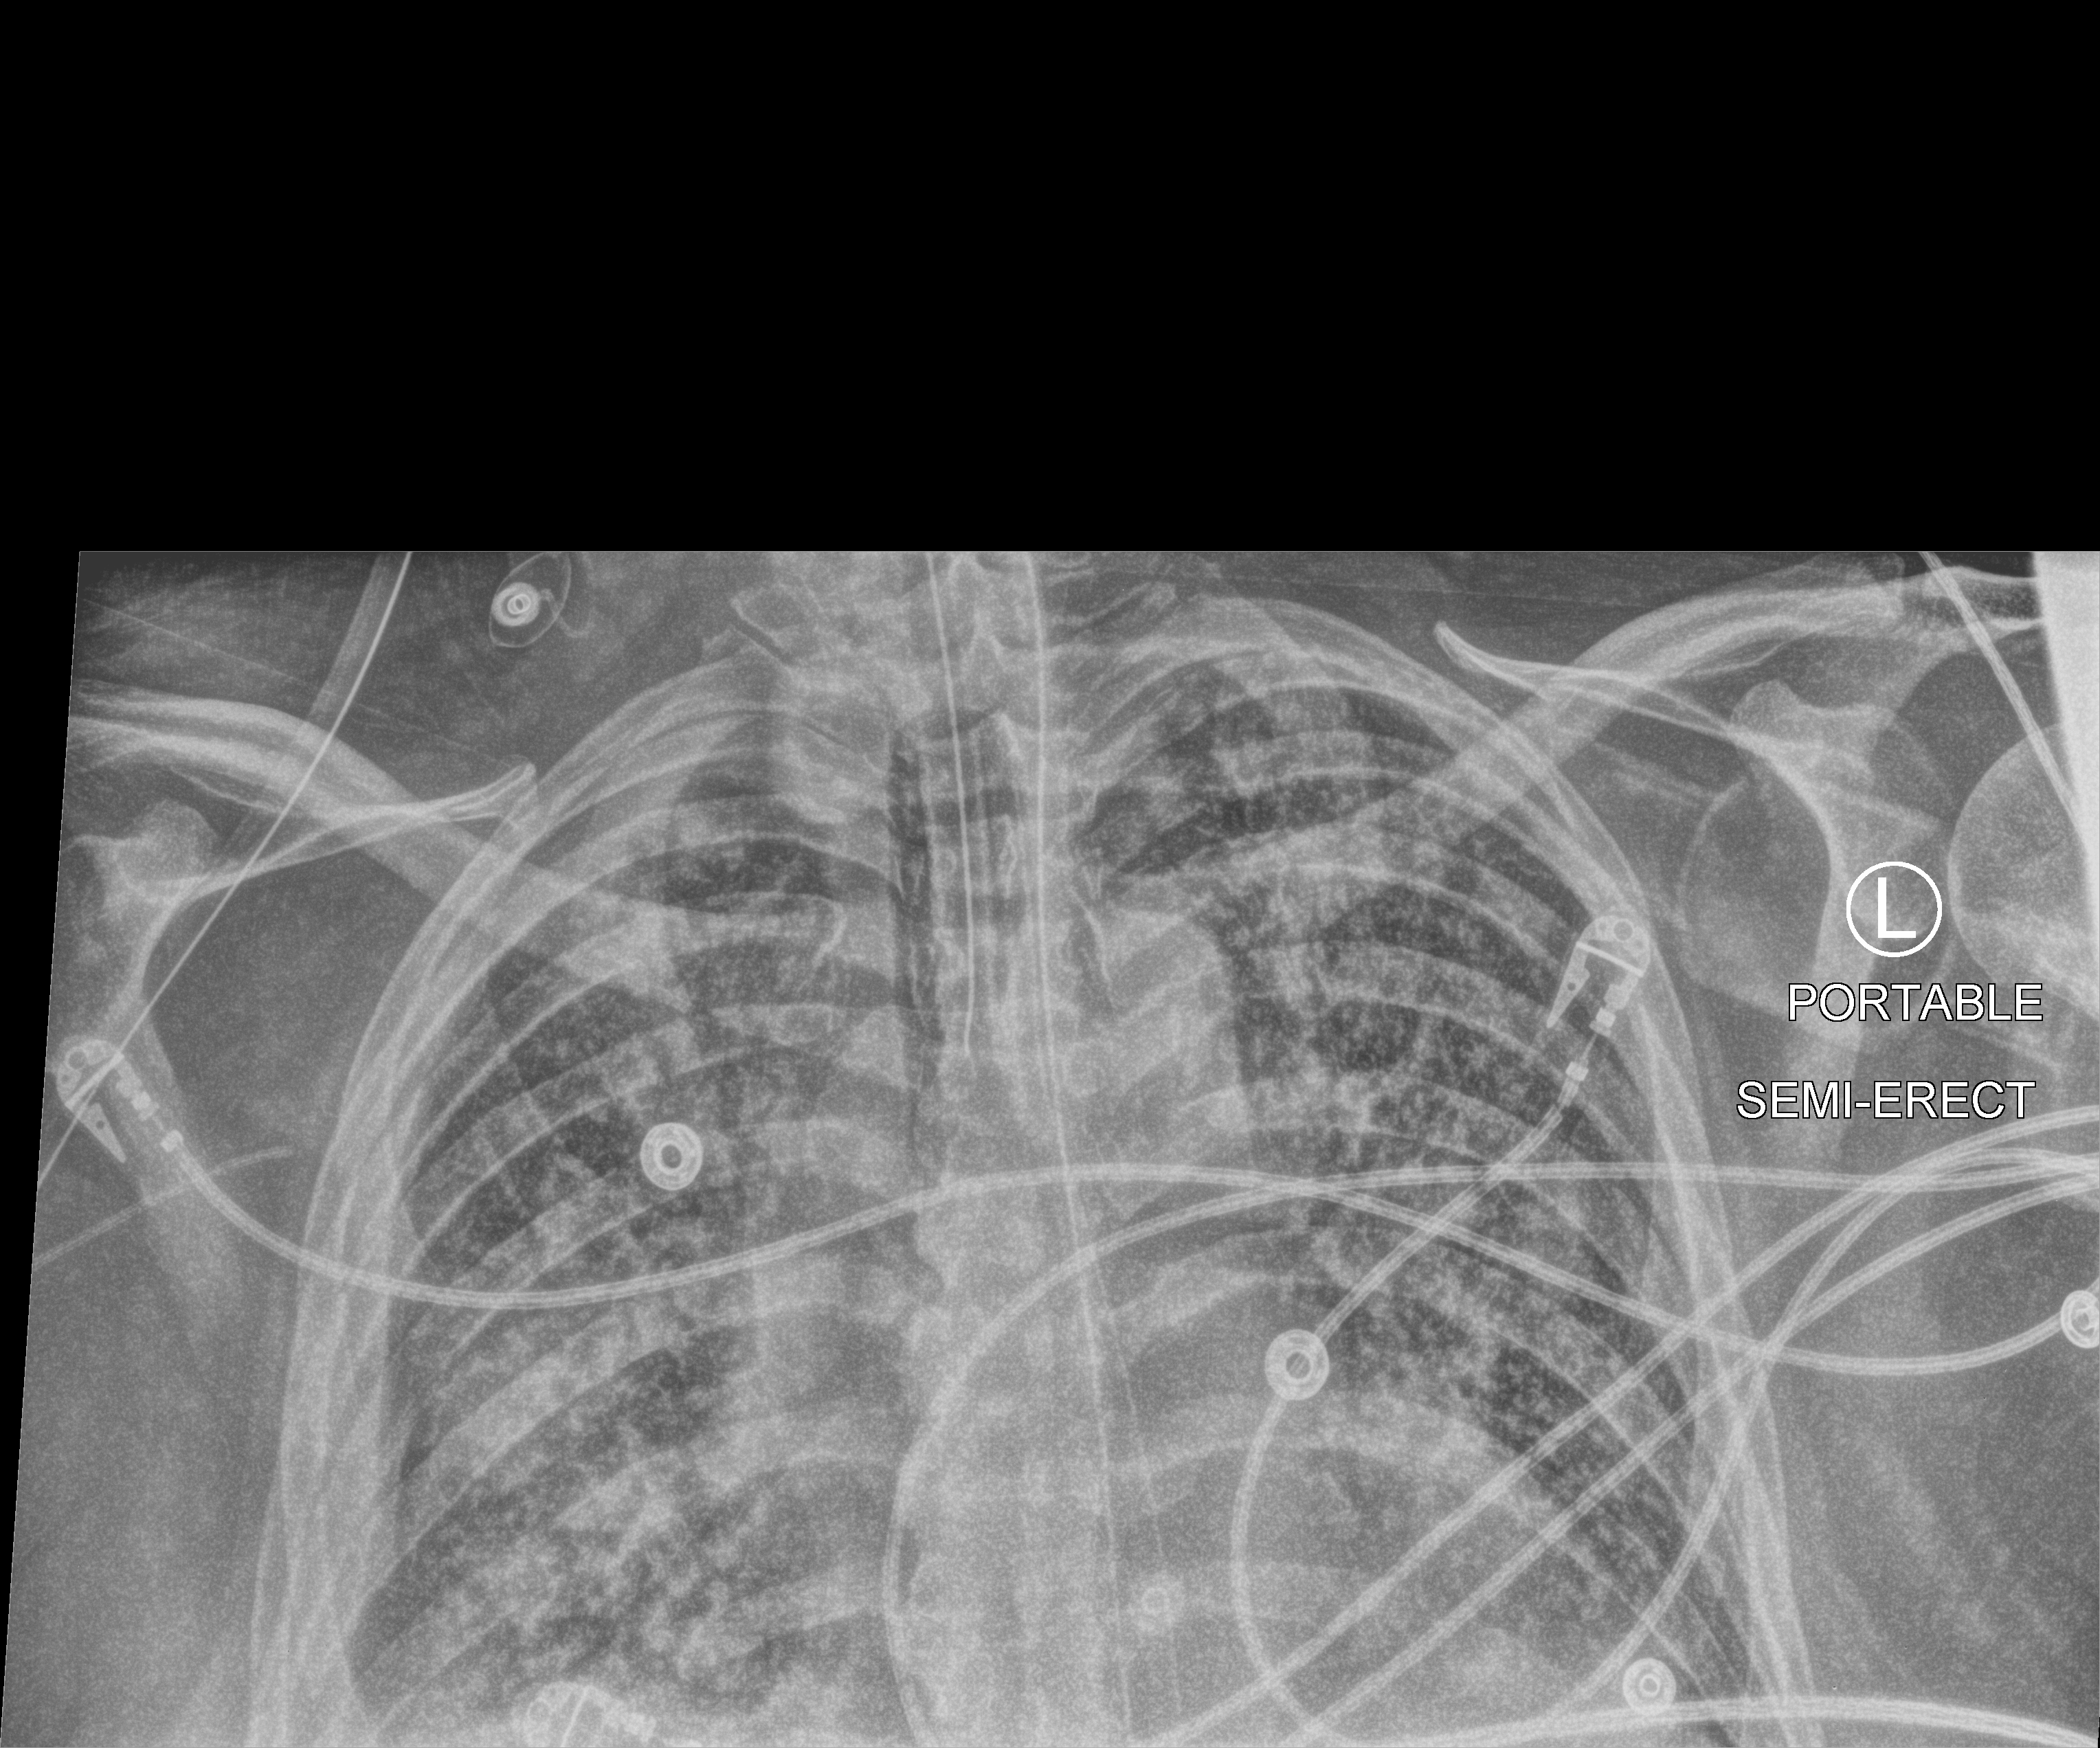
Bedside chest radiograph (computed radiography). Patient hospitalised with COVID-19; male, aged 60–74 years.
Hospital-stay facts (about this admission, not read from this image; timing relative to this image not recorded):
- mechanically ventilated during this hospital stay: yes
- length of hospital stay: 40 days